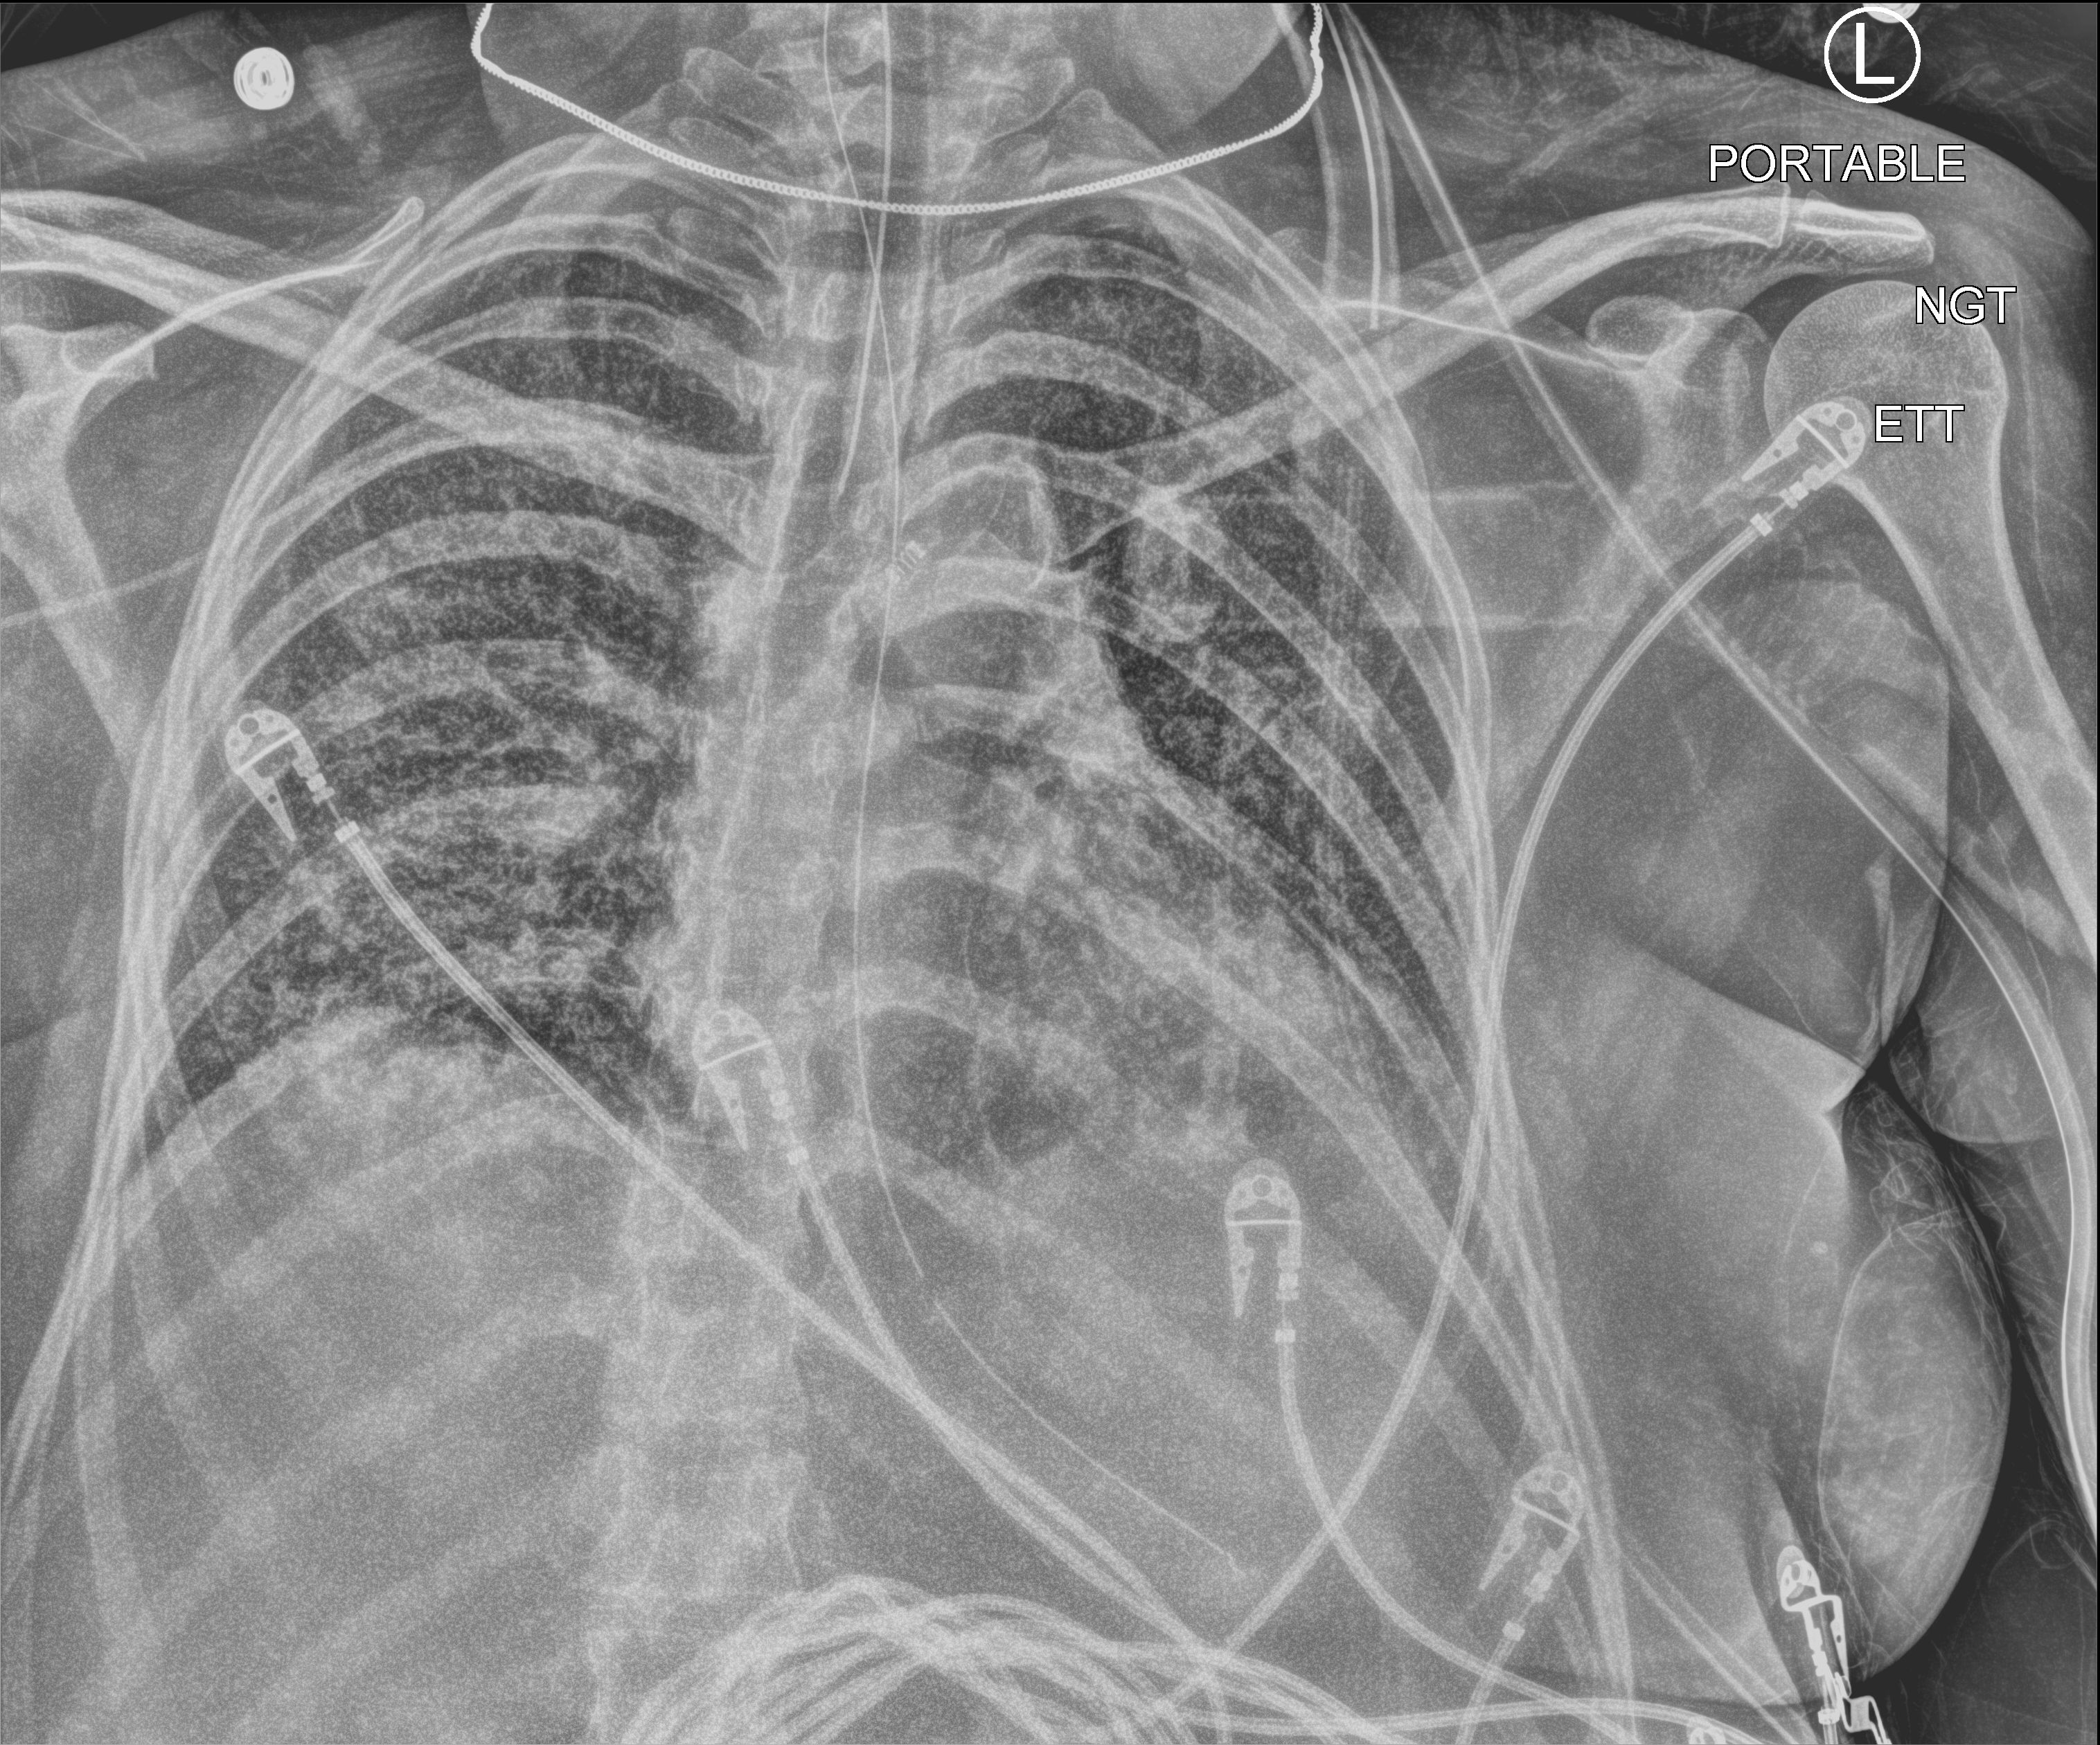
Chest X-ray (portable); anteroposterior (AP) projection. Patient hospitalised with COVID-19; female, aged 18–59 years.
From the hospital-stay record, not from the radiograph (when in the stay this image was taken is not recorded):
- length of hospital stay: 73 days